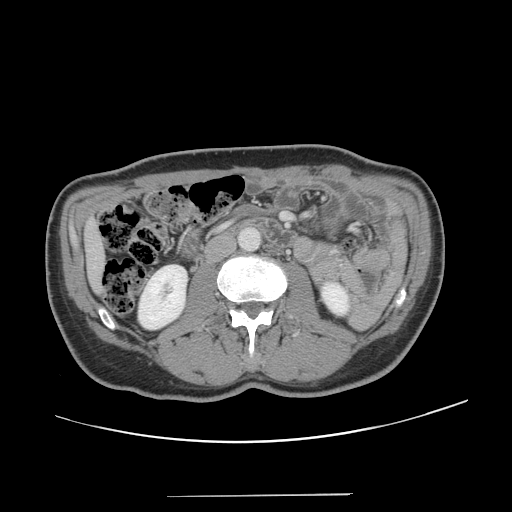
Contrast-enhanced abdominal CT, one axial slice; position 42 of 131 along the scan axis; 120 kVp; intravenous contrast given; soft-tissue window (W 400 / L 40 HU); 512 × 512 image matrix, field of view 403 × 403 mm. Male patient, age 60 years. From the clinical record (not read from this slice): diagnosis: colorectal cancer liver metastases, imaged before liver resection; multiple liver metastases: no; largest metastasis: 2.5 cm; chemotherapy before resection: no.
Structures marked on this image (outlined manually by an expert reader):
- liver: bounding box (x1, y1, x2, y2) in pixels: (86, 224, 103, 290)
- planned liver remnant (the part of the liver to remain after resection): (86, 224, 103, 290)